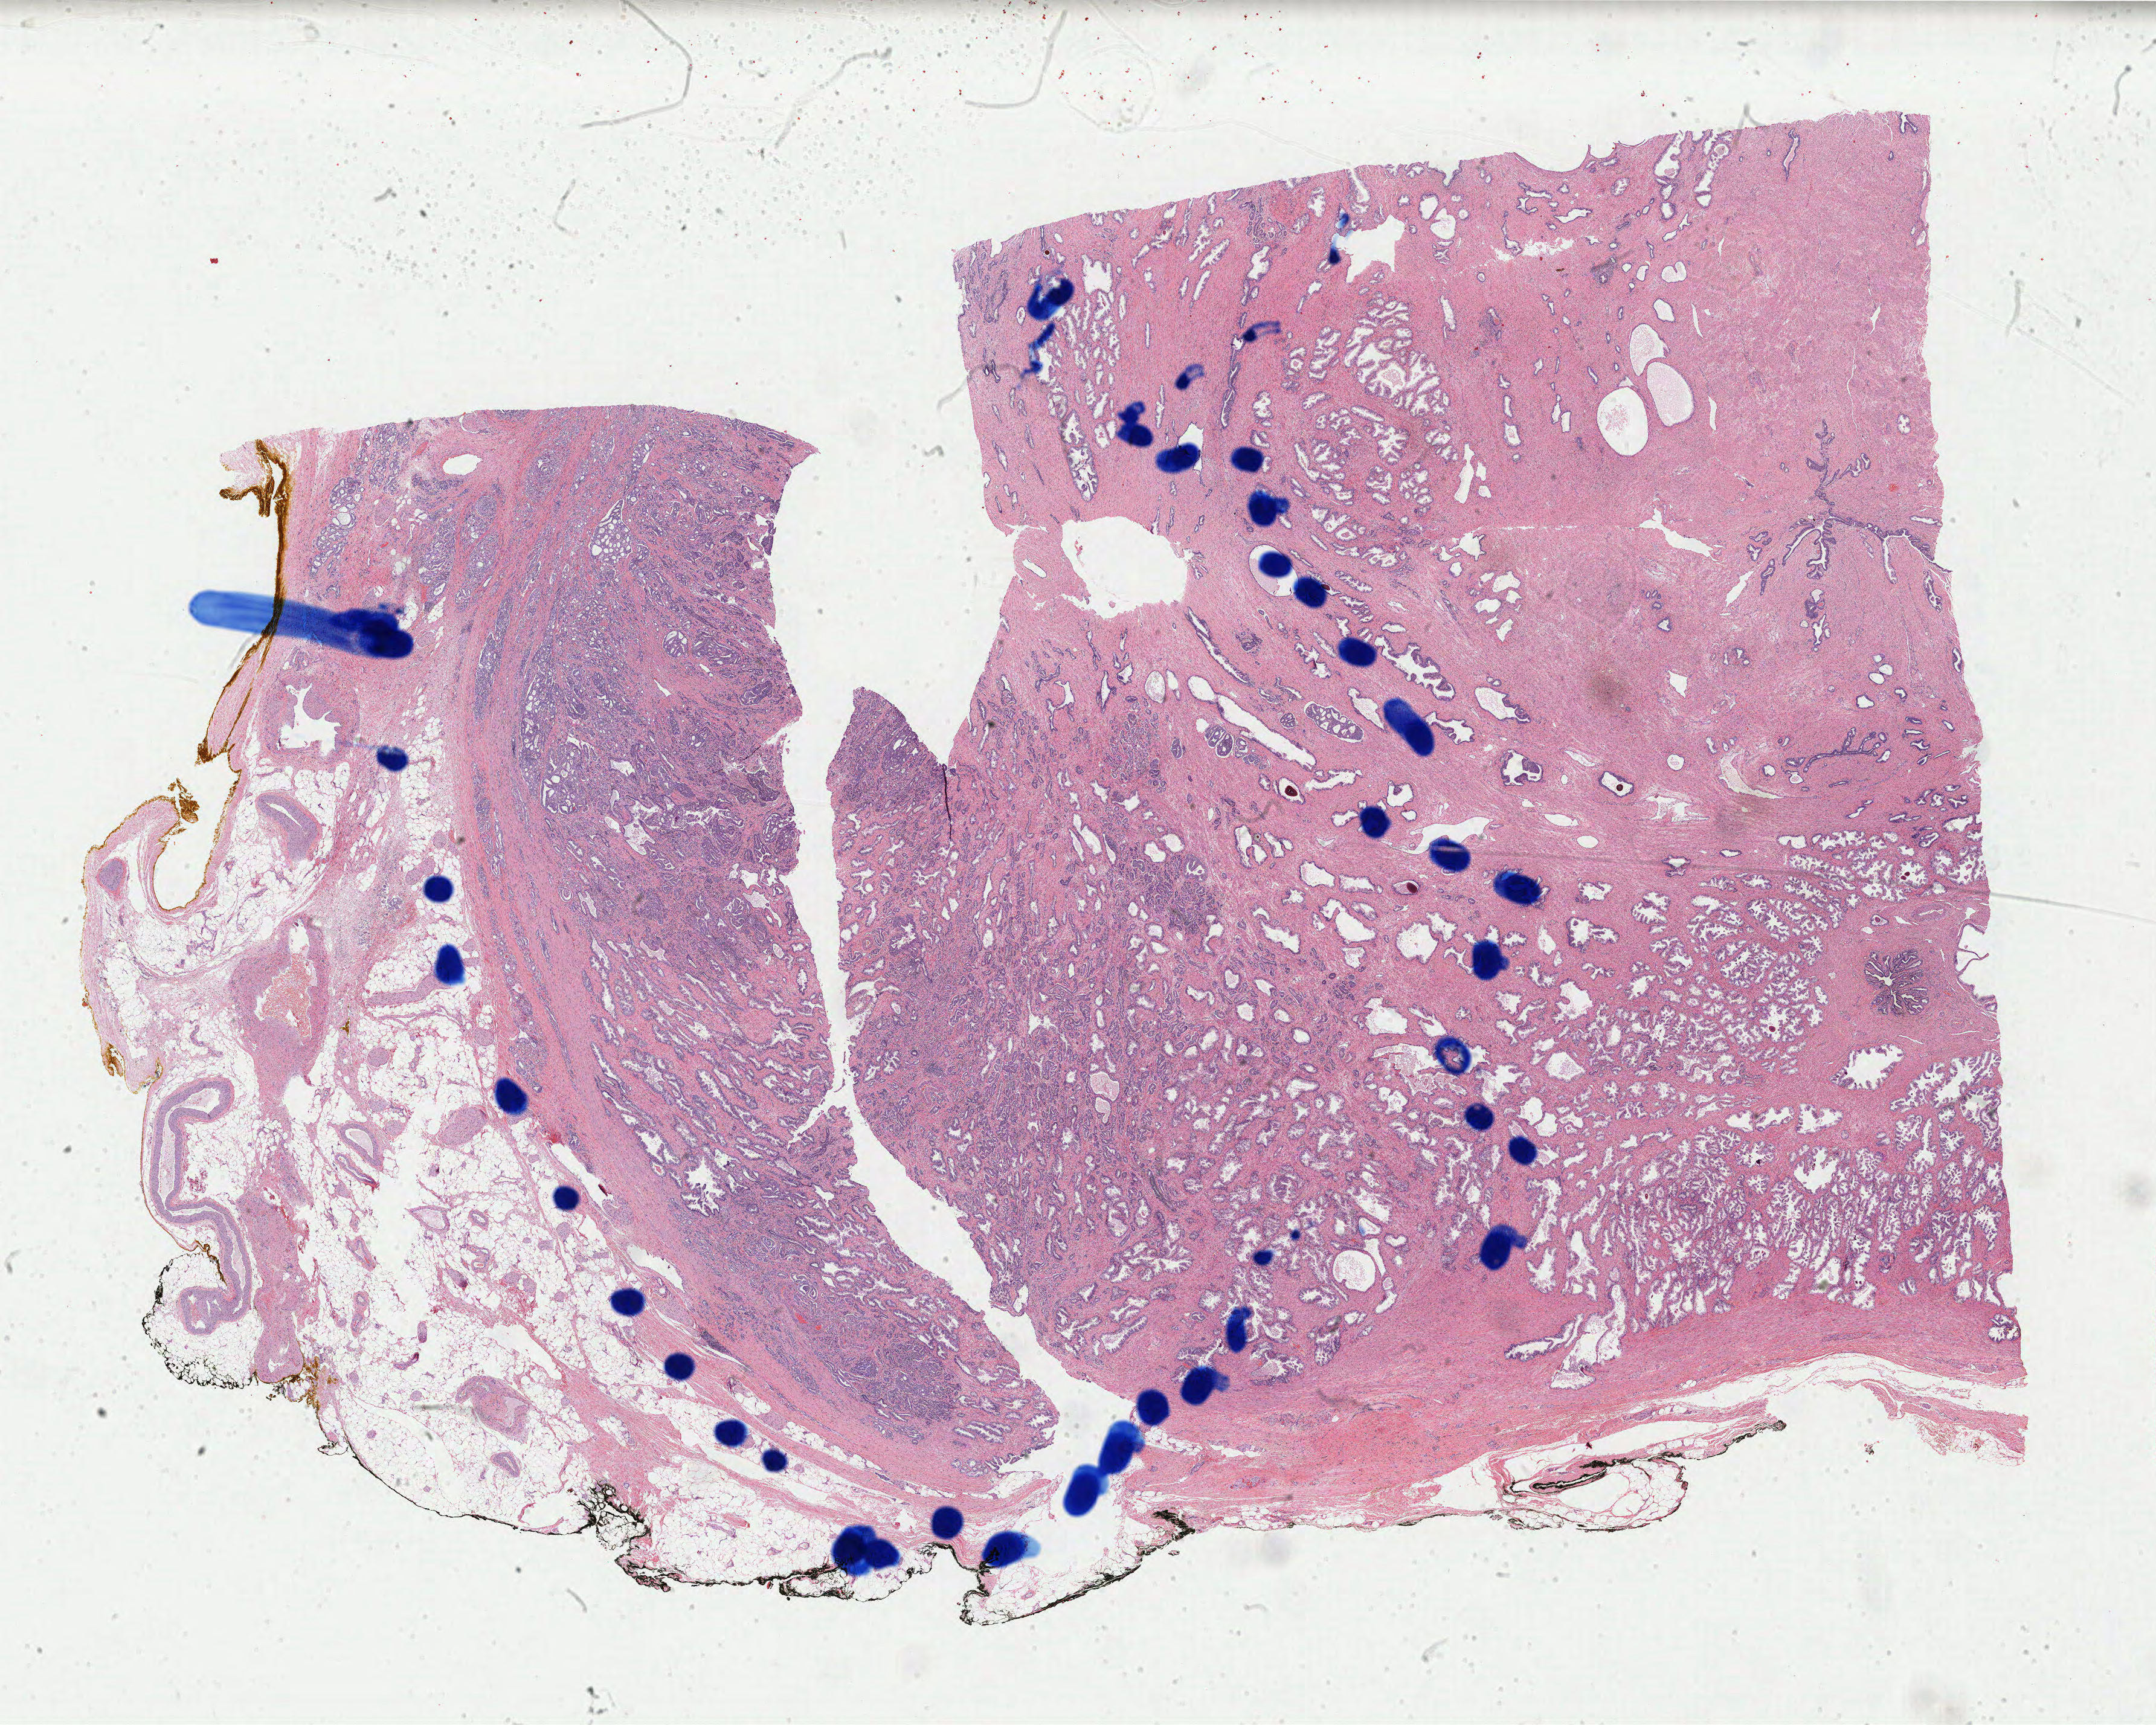
Hematoxylin and eosin (H&E) stained whole-slide image — a low-resolution overview of the entire scanned area, about 28.3 x 22.7 mm. Formalin-fixed paraffin-embedded (FFPE) diagnostic section. Primary tumour sample from the prostate. Male, age 56 years at initial diagnosis. Gleason score: 7 (4+3).
• pathologic diagnosis: Adenocarcinoma, NOS (prostate gland)